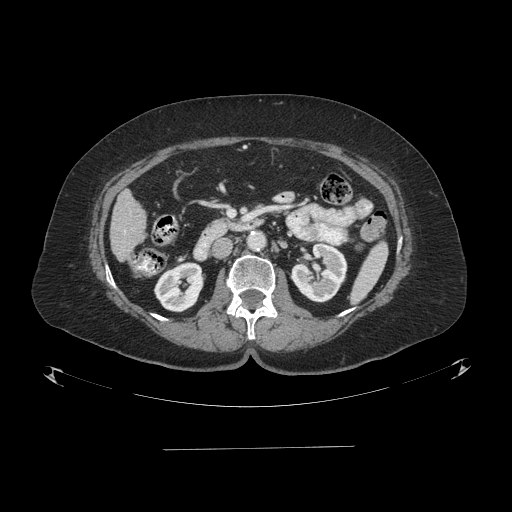
Contrast-enhanced abdominal CT (liver protocol), one axial slice; position 25 of 103 along the scan axis; 120 kVp; one of 2 acquisitions stored at this slice position; soft-tissue window (W 400 / L 40 HU); 2.5 mm slice thickness; 512 × 512 image matrix. From the clinical record (not read from this slice): diagnosis: hepatocellular carcinoma (patient treated with transarterial chemoembolisation; whether this scan precedes or follows treatment is not stated here); TNM stage (as recorded): Stage-IIIA; Child-Pugh class: A; tumour nodularity: multinodular.
Outlined on this slice (semi-automatically segmented with operator editing):
- liver parenchyma outside the tumour (the mass and vessels are separate outlines, so this box may not span the whole liver): box from (x=110, y=190) to (x=146, y=260) px